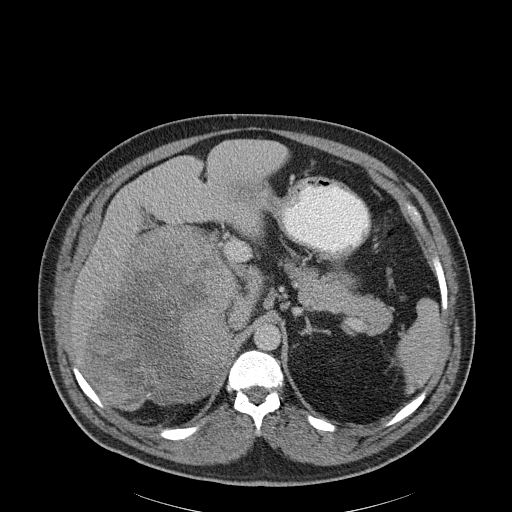
Contrast-enhanced abdominal CT, one axial slice; position 138 of 186 along the scan axis; soft-tissue window (W 400 / L 40 HU); 3 mm slice thickness; 512 × 512 image matrix, field of view 464 × 464 mm. Male patient, age 56 years. Case-level facts recorded for this patient, not image findings: diagnosis: adrenocortical carcinoma; tumour side: right adrenal; tumour size at pathology: 18 cm; Ki-67 index: 2 %; stage (as recorded): 3.
Annotated regions visible in this slice (semi-automatic segmentation, software-assisted and operator-edited):
- mass: bounding box (x1, y1, x2, y2) in pixels: (87, 226, 233, 409)